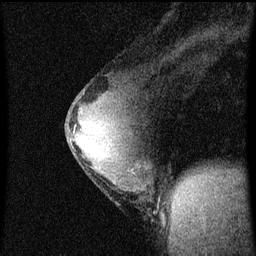
Breast MRI (dynamic contrast-enhanced), one sagittal slice. Position 35 of 60 along the scan axis. Dynamic contrast-enhanced series, image 2 of 4 at this slice position (ordered by acquisition). 1.5 T. TE 4.2 ms, TR 8 ms. 256 × 256 image matrix, field of view 180 × 180 mm. Patient: female, 33 years.
Structures marked on this image (semi-automatic segmentation, software-assisted and operator-edited):
- analysis volume of interest (the breast-tissue region the enhancement analysis was run in; not a lesion): box from (x=66, y=76) to (x=152, y=217) px
- tumour enhancement mask (voxels above the 70 % enhancement threshold inside the analysis volume of interest): (x=73, y=116)–(x=83, y=149)